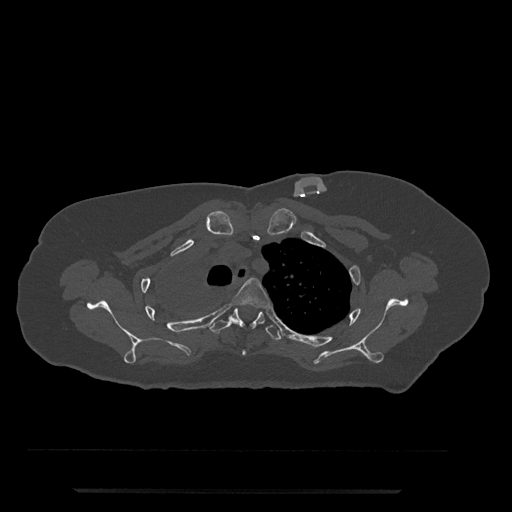
CT including the spine, one axial slice. Slice 611 of 797 in the series (ordered by position). Reconstruction kernel Br40s/3. 120 kVp. Bone window (W 1800 / L 400 HU). 0.5 mm slice thickness. 512 × 512 image matrix, field of view 440 × 440 mm. Female patient, age 51 years. Case-level facts recorded for this patient, not image findings: primary cancer: neuro; vertebrae with lytic lesions (as recorded): T8.
Annotated regions visible in this slice (semi-automatically segmented with operator editing):
- T3 vertebra: bounding box <231,278,270,355> (left, top, right, bottom; pixels)
- T4 vertebra: <209,308,281,341>